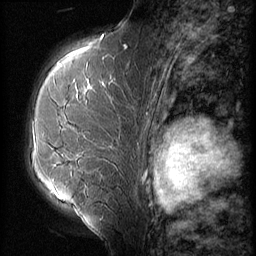
Breast MRI (dynamic contrast-enhanced), one sagittal slice. Slice 39 of 56 in the series (ordered by position). 3 images stored at this slice position (order not interpretable as contrast timing). 1.5 T. TE 4.2 ms, TR 9 ms. 2.5 mm slice thickness. 256 × 256 image matrix, field of view 180 × 180 mm. Female patient, age 51 years. Case-level facts recorded for this patient, not image findings: setting: breast cancer imaged before/during neoadjuvant chemotherapy; receptor status: HR-positive, HER2-negative.
Outlined on this slice (semi-automatic segmentation, software-assisted and operator-edited):
- analysis volume of interest (the breast-tissue region the enhancement analysis was run in; not a lesion): box from (x=24, y=56) to (x=141, y=165) px
- tumour enhancement mask (voxels above the 140 % enhancement threshold inside the analysis volume of interest): (x=85, y=80)–(x=113, y=91)